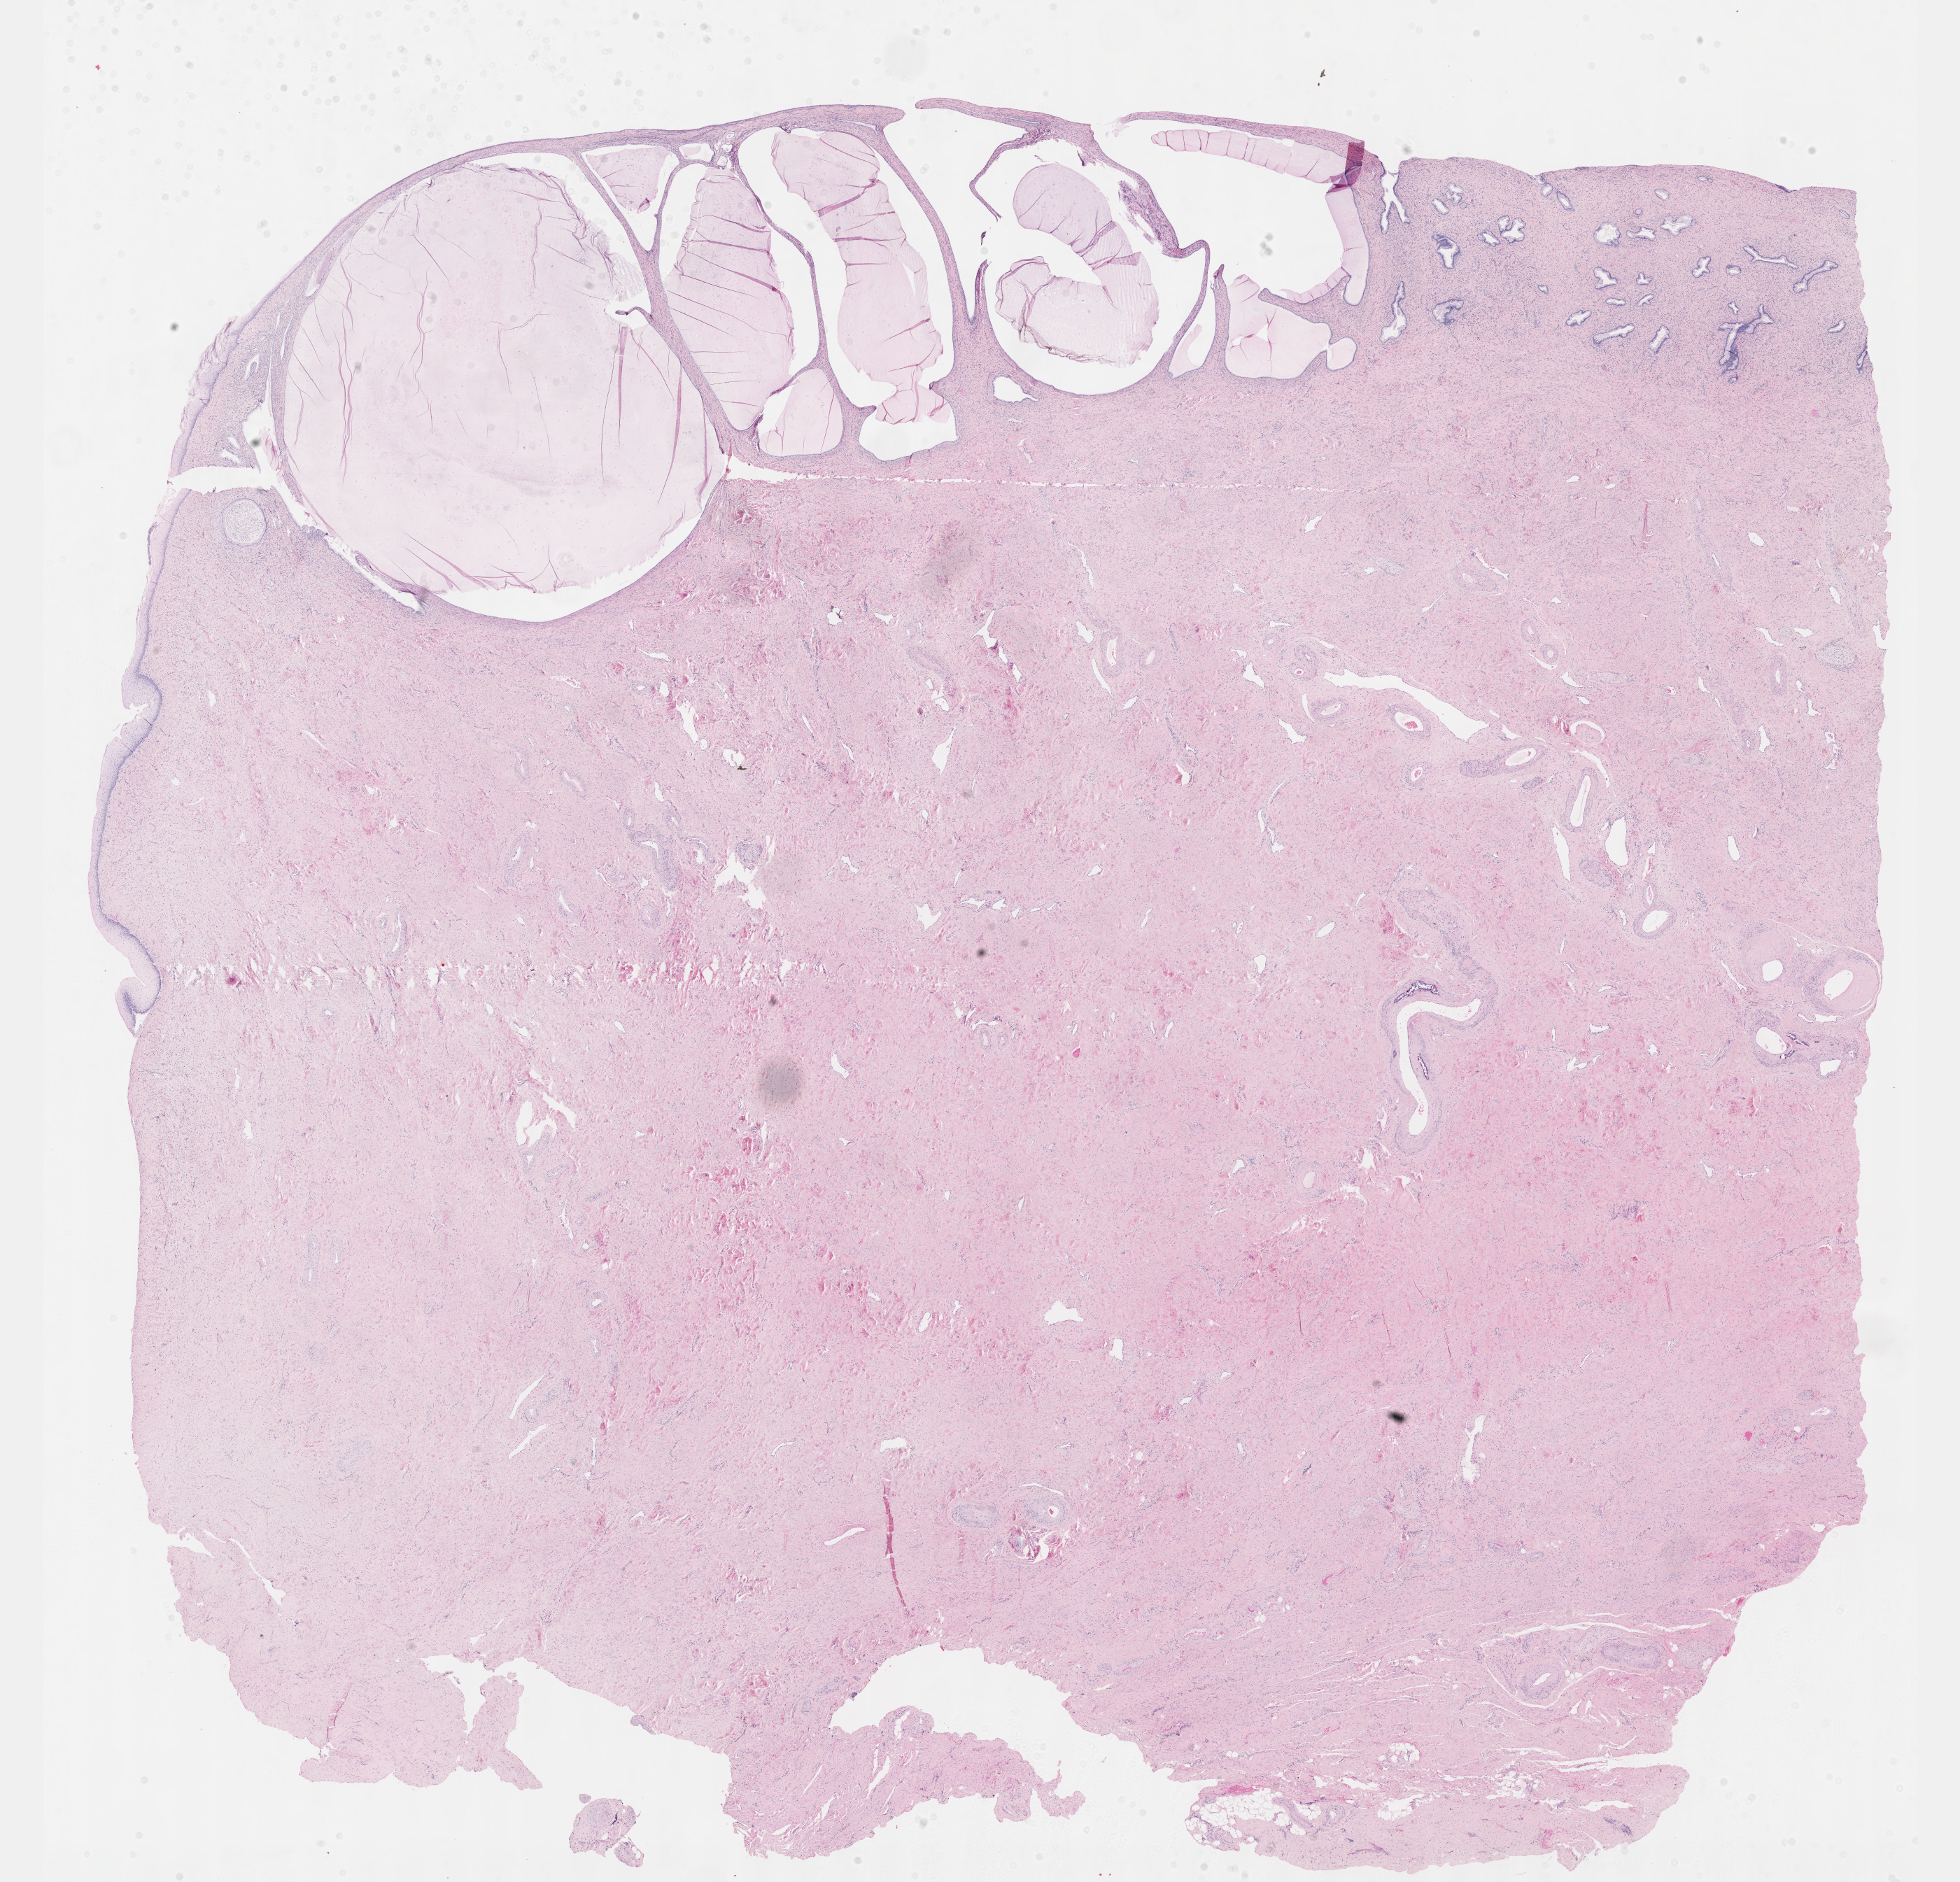
Digitized H&E tissue section (whole slide) — a low-resolution overview of the entire scanned area, about 22.6 x 21.7 mm, formalin-fixed paraffin-embedded (FFPE) diagnostic section, sample: primary tumour, uterus. Patient: female, age at initial diagnosis 73 years. Histologic grade: G3 (poorly differentiated).
* FIGO stage: IA
* histologic diagnosis: Serous surface papillary carcinoma (endometrium)